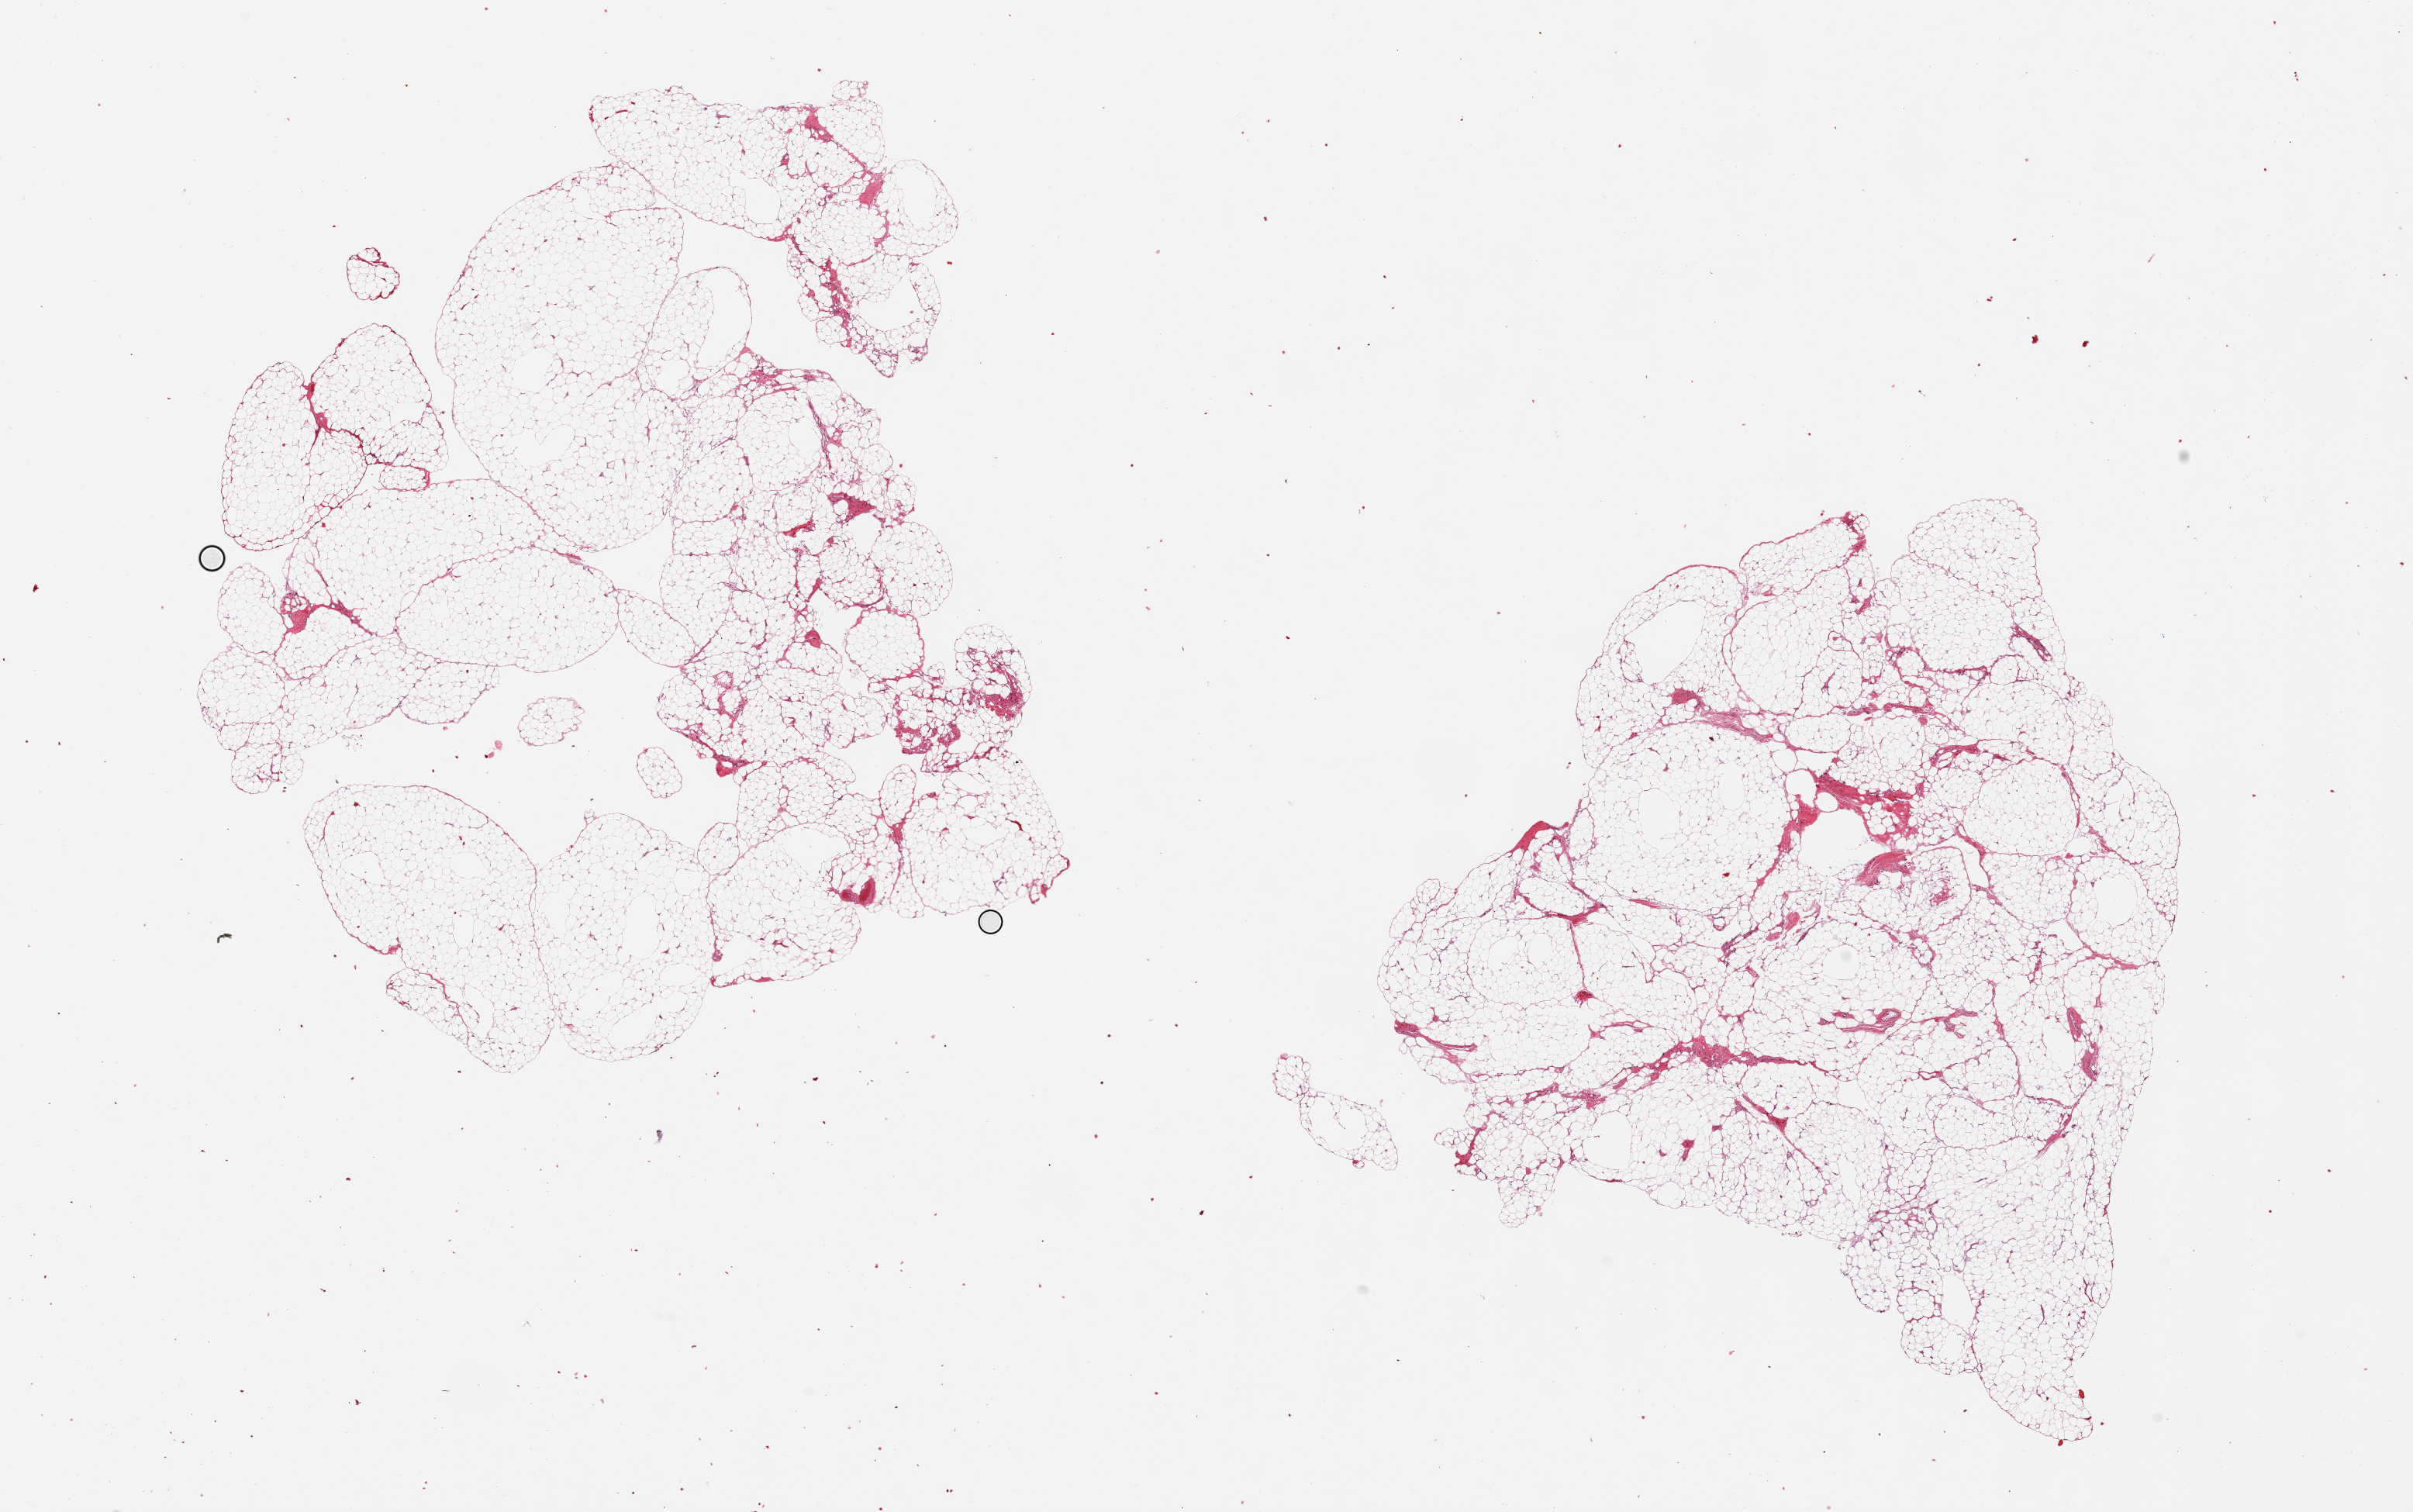
Hematoxylin and eosin (H&E) whole-slide image, low-resolution overview of the scanned area, about 24.6 x 15.4 mm. PAXgene-fixed paraffin-embedded (PFPE) section. Sampled site (target tissue): omentum. Tissue donor sample. Male donor.
- reviewer comment on this tissue sample: 2 pieces ~8x6mm